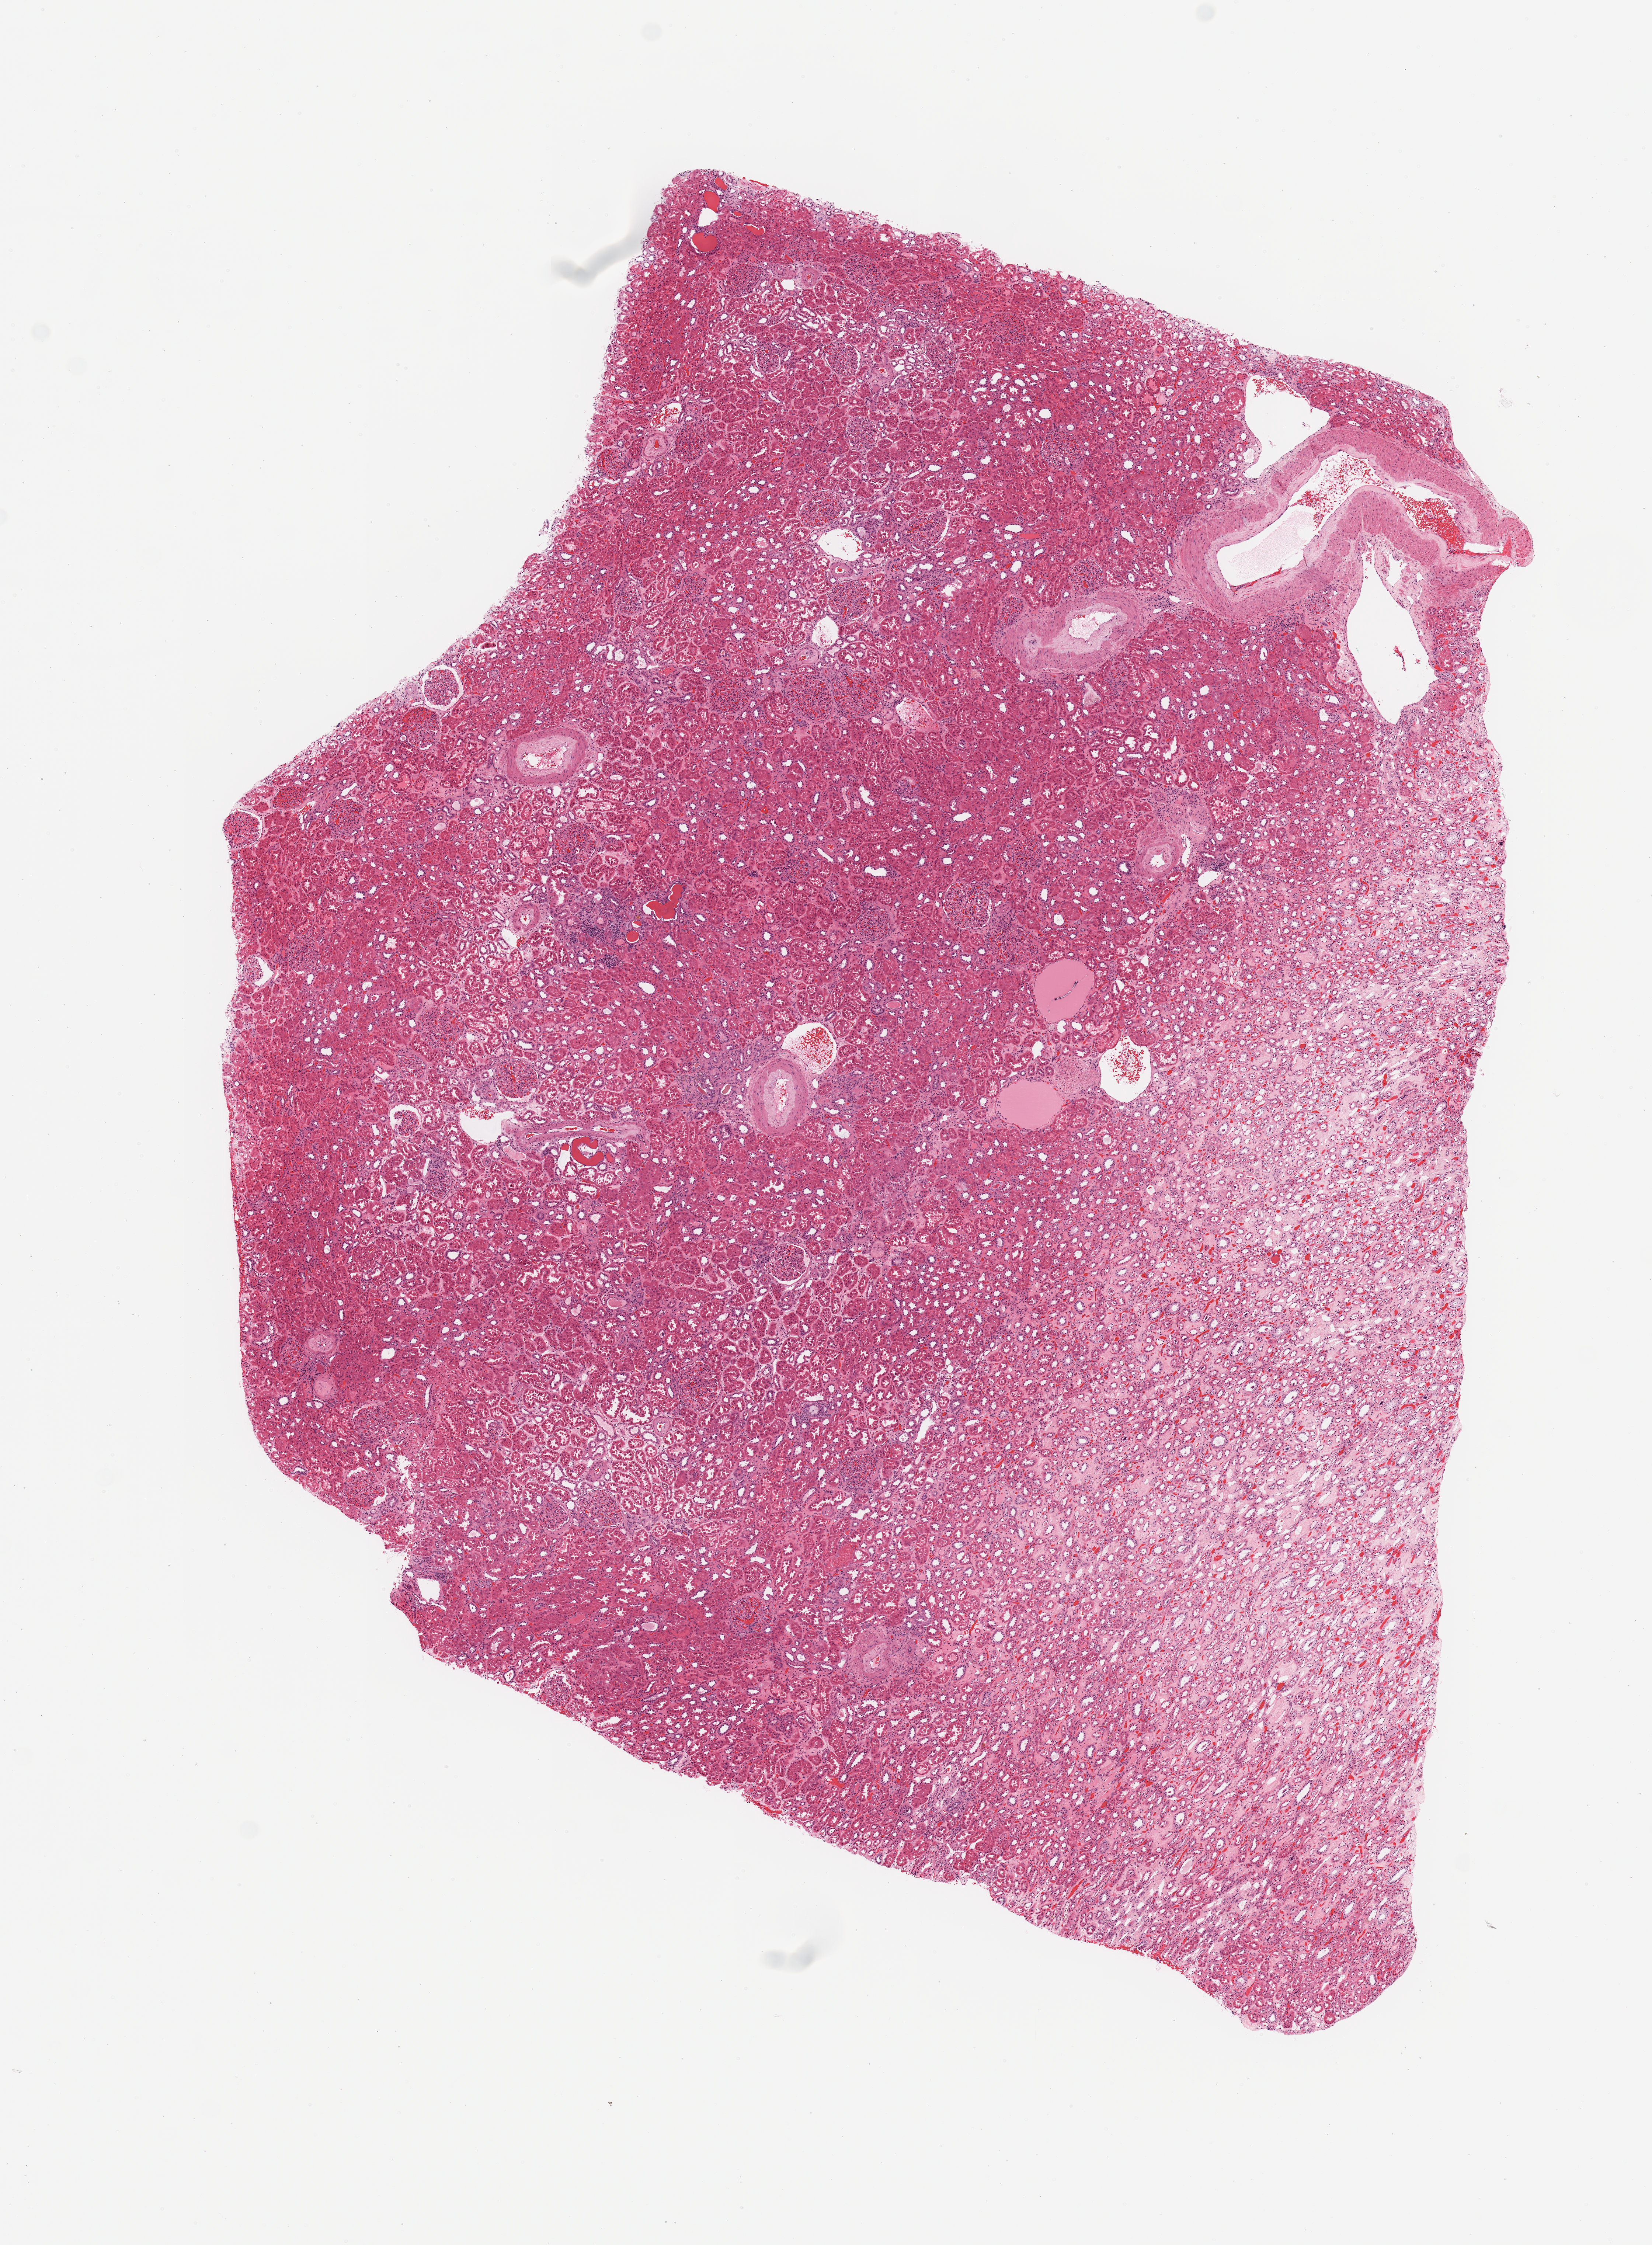
Whole-slide histology image, H&E — whole scanned area (about 8.9 x 12.0 mm, slide scanned at 20x) shown as a low-resolution overview. Normal (non-tumour) tissue sample, sampled site: kidney. Patient: male, age 66 years.
This section: normal (non-tumour) tissue from the same patient. Patient diagnosis: Renal cell carcinoma, NOS.